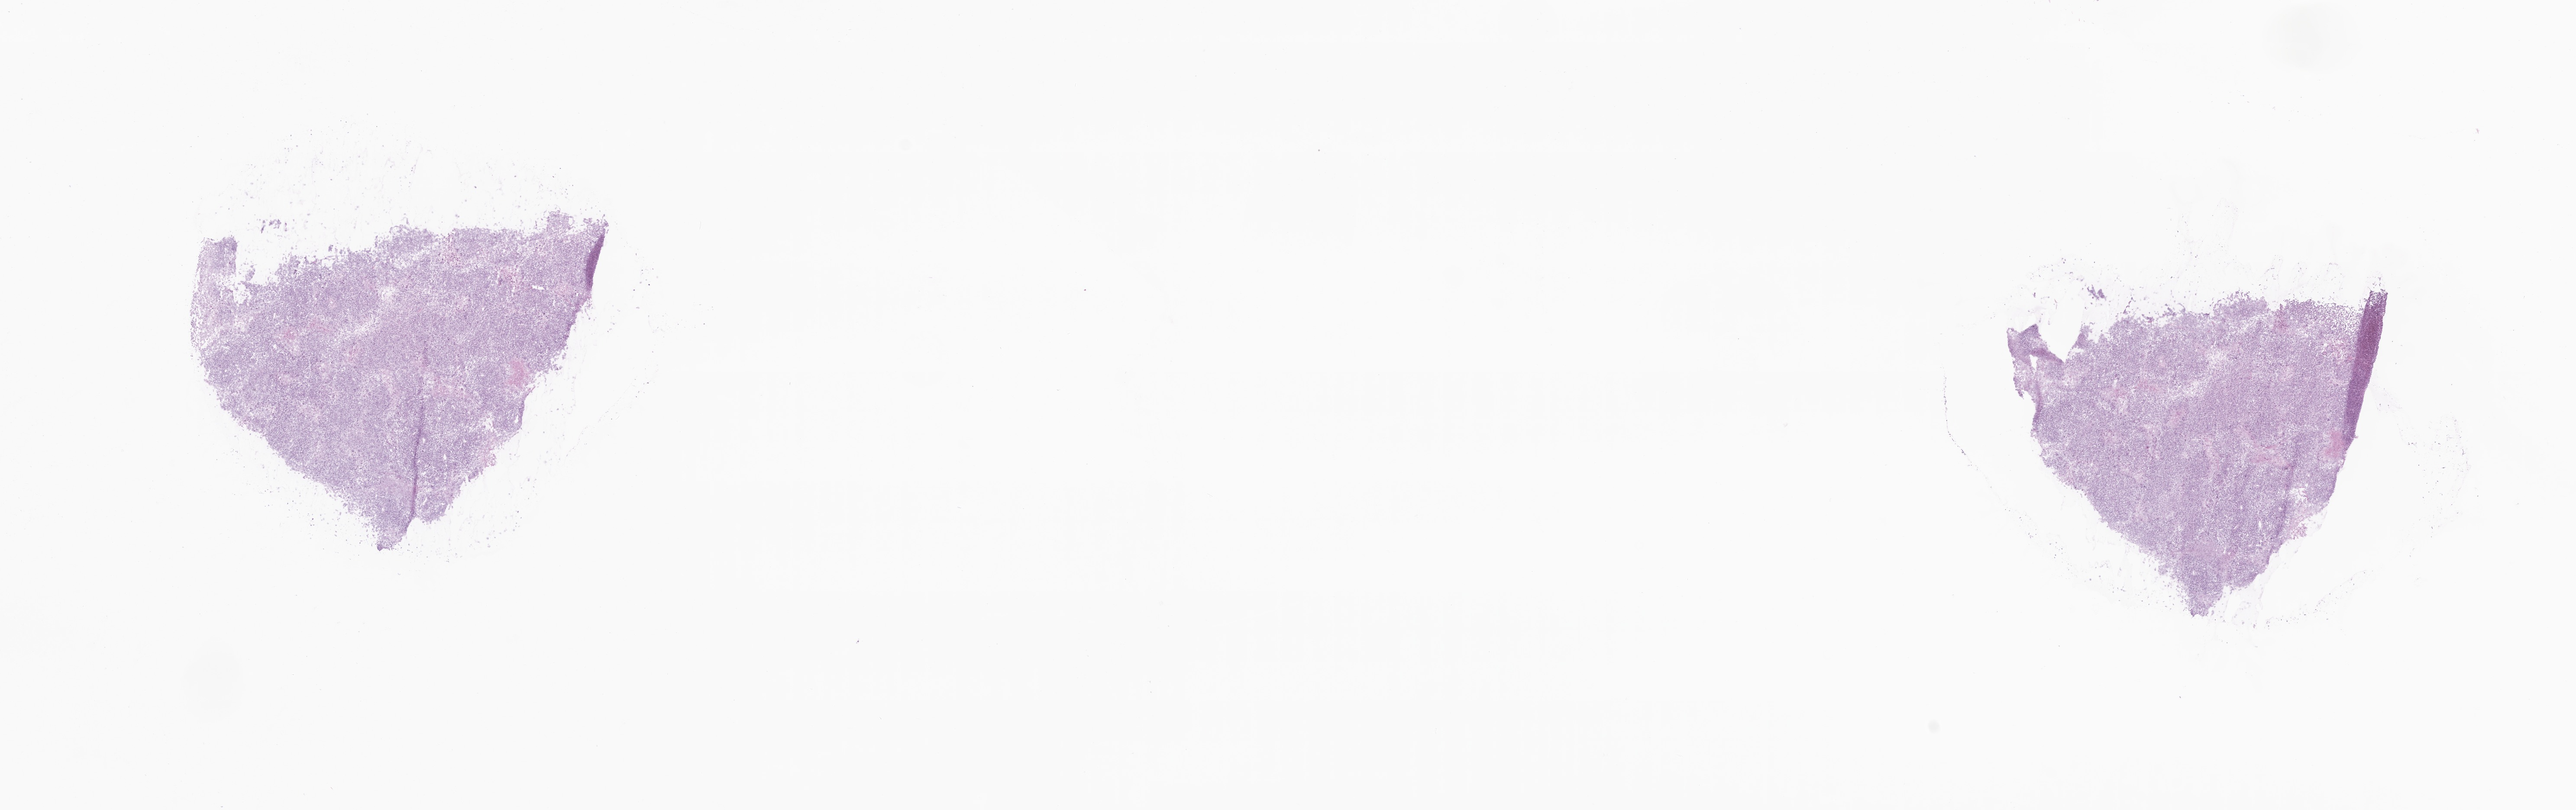
Digitized hematoxylin and eosin (H&E)-stained section — a low-resolution overview of the entire scanned area, about 25.1 x 7.9 mm, frozen section, metastatic tumor tissue, resected from skin. Patient: male, age at initial diagnosis 75 years. Pathologist review of this section (percent, as recorded): tumor cells 90%, tumor nuclei 90%, stromal cells 10%, necrosis 0%, normal cells 0%. Infiltration values recorded for this section: lymphocyte infiltration 0%, monocyte infiltration 0%, neutrophil infiltration 0%.
* section: top of the tissue portion
* patient diagnosis (primary): Malignant melanoma, NOS